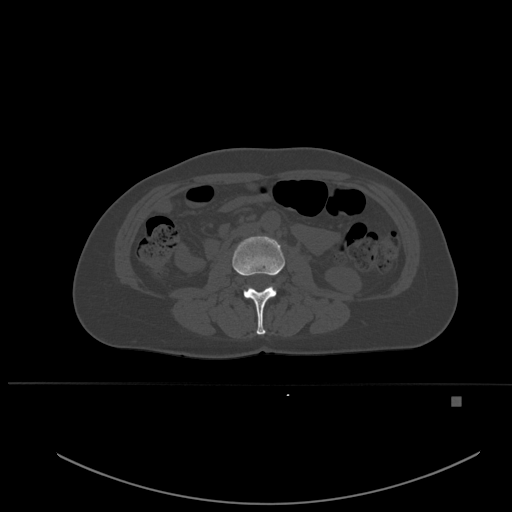
CT including the spine, one axial slice. Bone window (W 1800 / L 400 HU). 1.5 mm slice thickness. 512 × 512 image matrix, field of view 443 × 443 mm. Female patient, age 49 years. Case-level facts recorded for this patient, not image findings: primary cancer: breast.
Structures marked on this image (semi-automatic segmentation, software-assisted and operator-edited):
- L2 vertebra: bounding box [x1, y1, x2, y2] px = [232, 236, 285, 335]